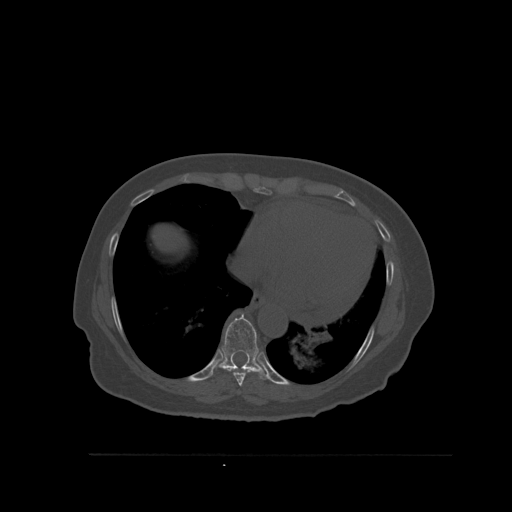
CT including the spine, one axial slice. Slice 340 of 527 in the series (ordered by position). Bone window (W 1800 / L 400 HU). 1.5 mm slice thickness. 512 × 512 image matrix, field of view 470 × 470 mm. Patient: female, 73 years. Case-level facts recorded for this patient, not image findings: primary cancer: breast; vertebrae with lytic lesions (as recorded): L2.
Outlined on this slice (semi-automatic segmentation, software-assisted and operator-edited):
- T8 vertebra: bounding box [x1, y1, x2, y2] px = [233, 369, 260, 387]
- T9 vertebra: [212, 313, 270, 380]